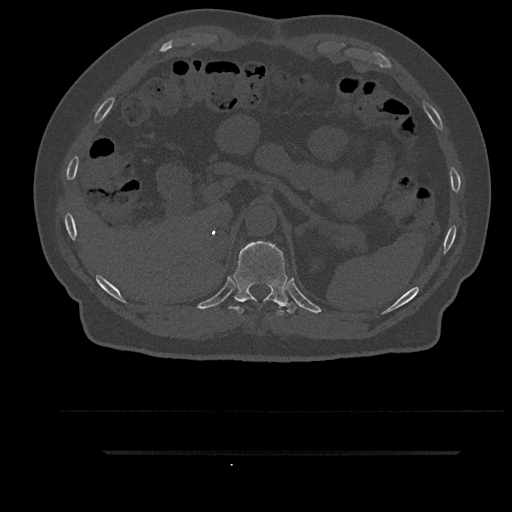
CT including the spine, one axial slice; position 319 of 797 along the scan axis; bone window (W 1800 / L 400 HU); 0.5 mm slice thickness; 512 × 512 image matrix, field of view 432 × 432 mm. Male patient, age 63 years. From the clinical record (not read from this slice): primary cancer: renal.
Structures marked on this image (semi-automatically segmented with operator editing):
- T11 vertebra: bounding box <229,241,296,315> (left, top, right, bottom; pixels)